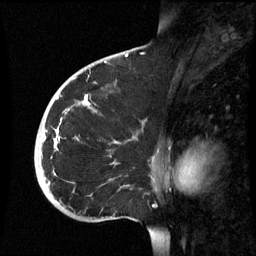
Breast MRI (dynamic contrast-enhanced), one sagittal slice; slice 37 of 60 in the series (ordered by position); dynamic contrast-enhanced series, image 2 of 3 at this slice position (ordered by acquisition); 1.5 T; TE 4.2 ms, TR 8.9 ms; 2.6 mm slice thickness; 256 × 256 image matrix, field of view 220 × 220 mm. Female patient, age 35 years. Case-level facts recorded for this patient, not image findings: setting: breast cancer imaged before/during neoadjuvant chemotherapy; receptor status: HR-positive, HER2-negative.
Outlined on this slice (semi-automatic segmentation, software-assisted and operator-edited):
- analysis volume of interest (the breast-tissue region the enhancement analysis was run in; not a lesion): bounding box (x1, y1, x2, y2) in pixels: (34, 74, 163, 221)
- tumour enhancement mask (voxels above the 70 % enhancement threshold inside the analysis volume of interest): (43, 96, 89, 147)